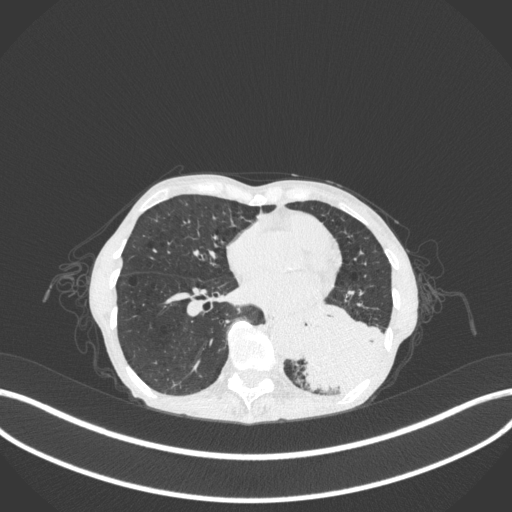
Chest CT, one axial slice. Position 103 of 347 along the scan axis. Reconstruction kernel B31f. Lung window (W 1500 / L -600 HU). 512 × 512 image matrix, field of view 400 × 400 mm. Patient: female, 70 years. From the clinical record (not read from this slice): clinical TNM (as recorded): T3 N0 M0.
Annotated regions visible in this slice (rectangle marked by the reading radiologist):
- lung tumour (recorded histology: small cell carcinoma): box from (x=295, y=291) to (x=395, y=396) px